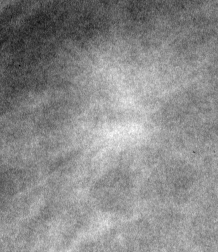
Region of interest cut from a scanned film mammogram (one marked finding), left breast, MLO view, BI-RADS breast density category 2 (scale 1–4).
Finding: mass, shape irregular, margins spiculated; BI-RADS assessment category 4; subtlety rating 1 on a 1 (subtle) to 5 (obvious) scale; pathology result (as recorded, not read from the image): malignant.